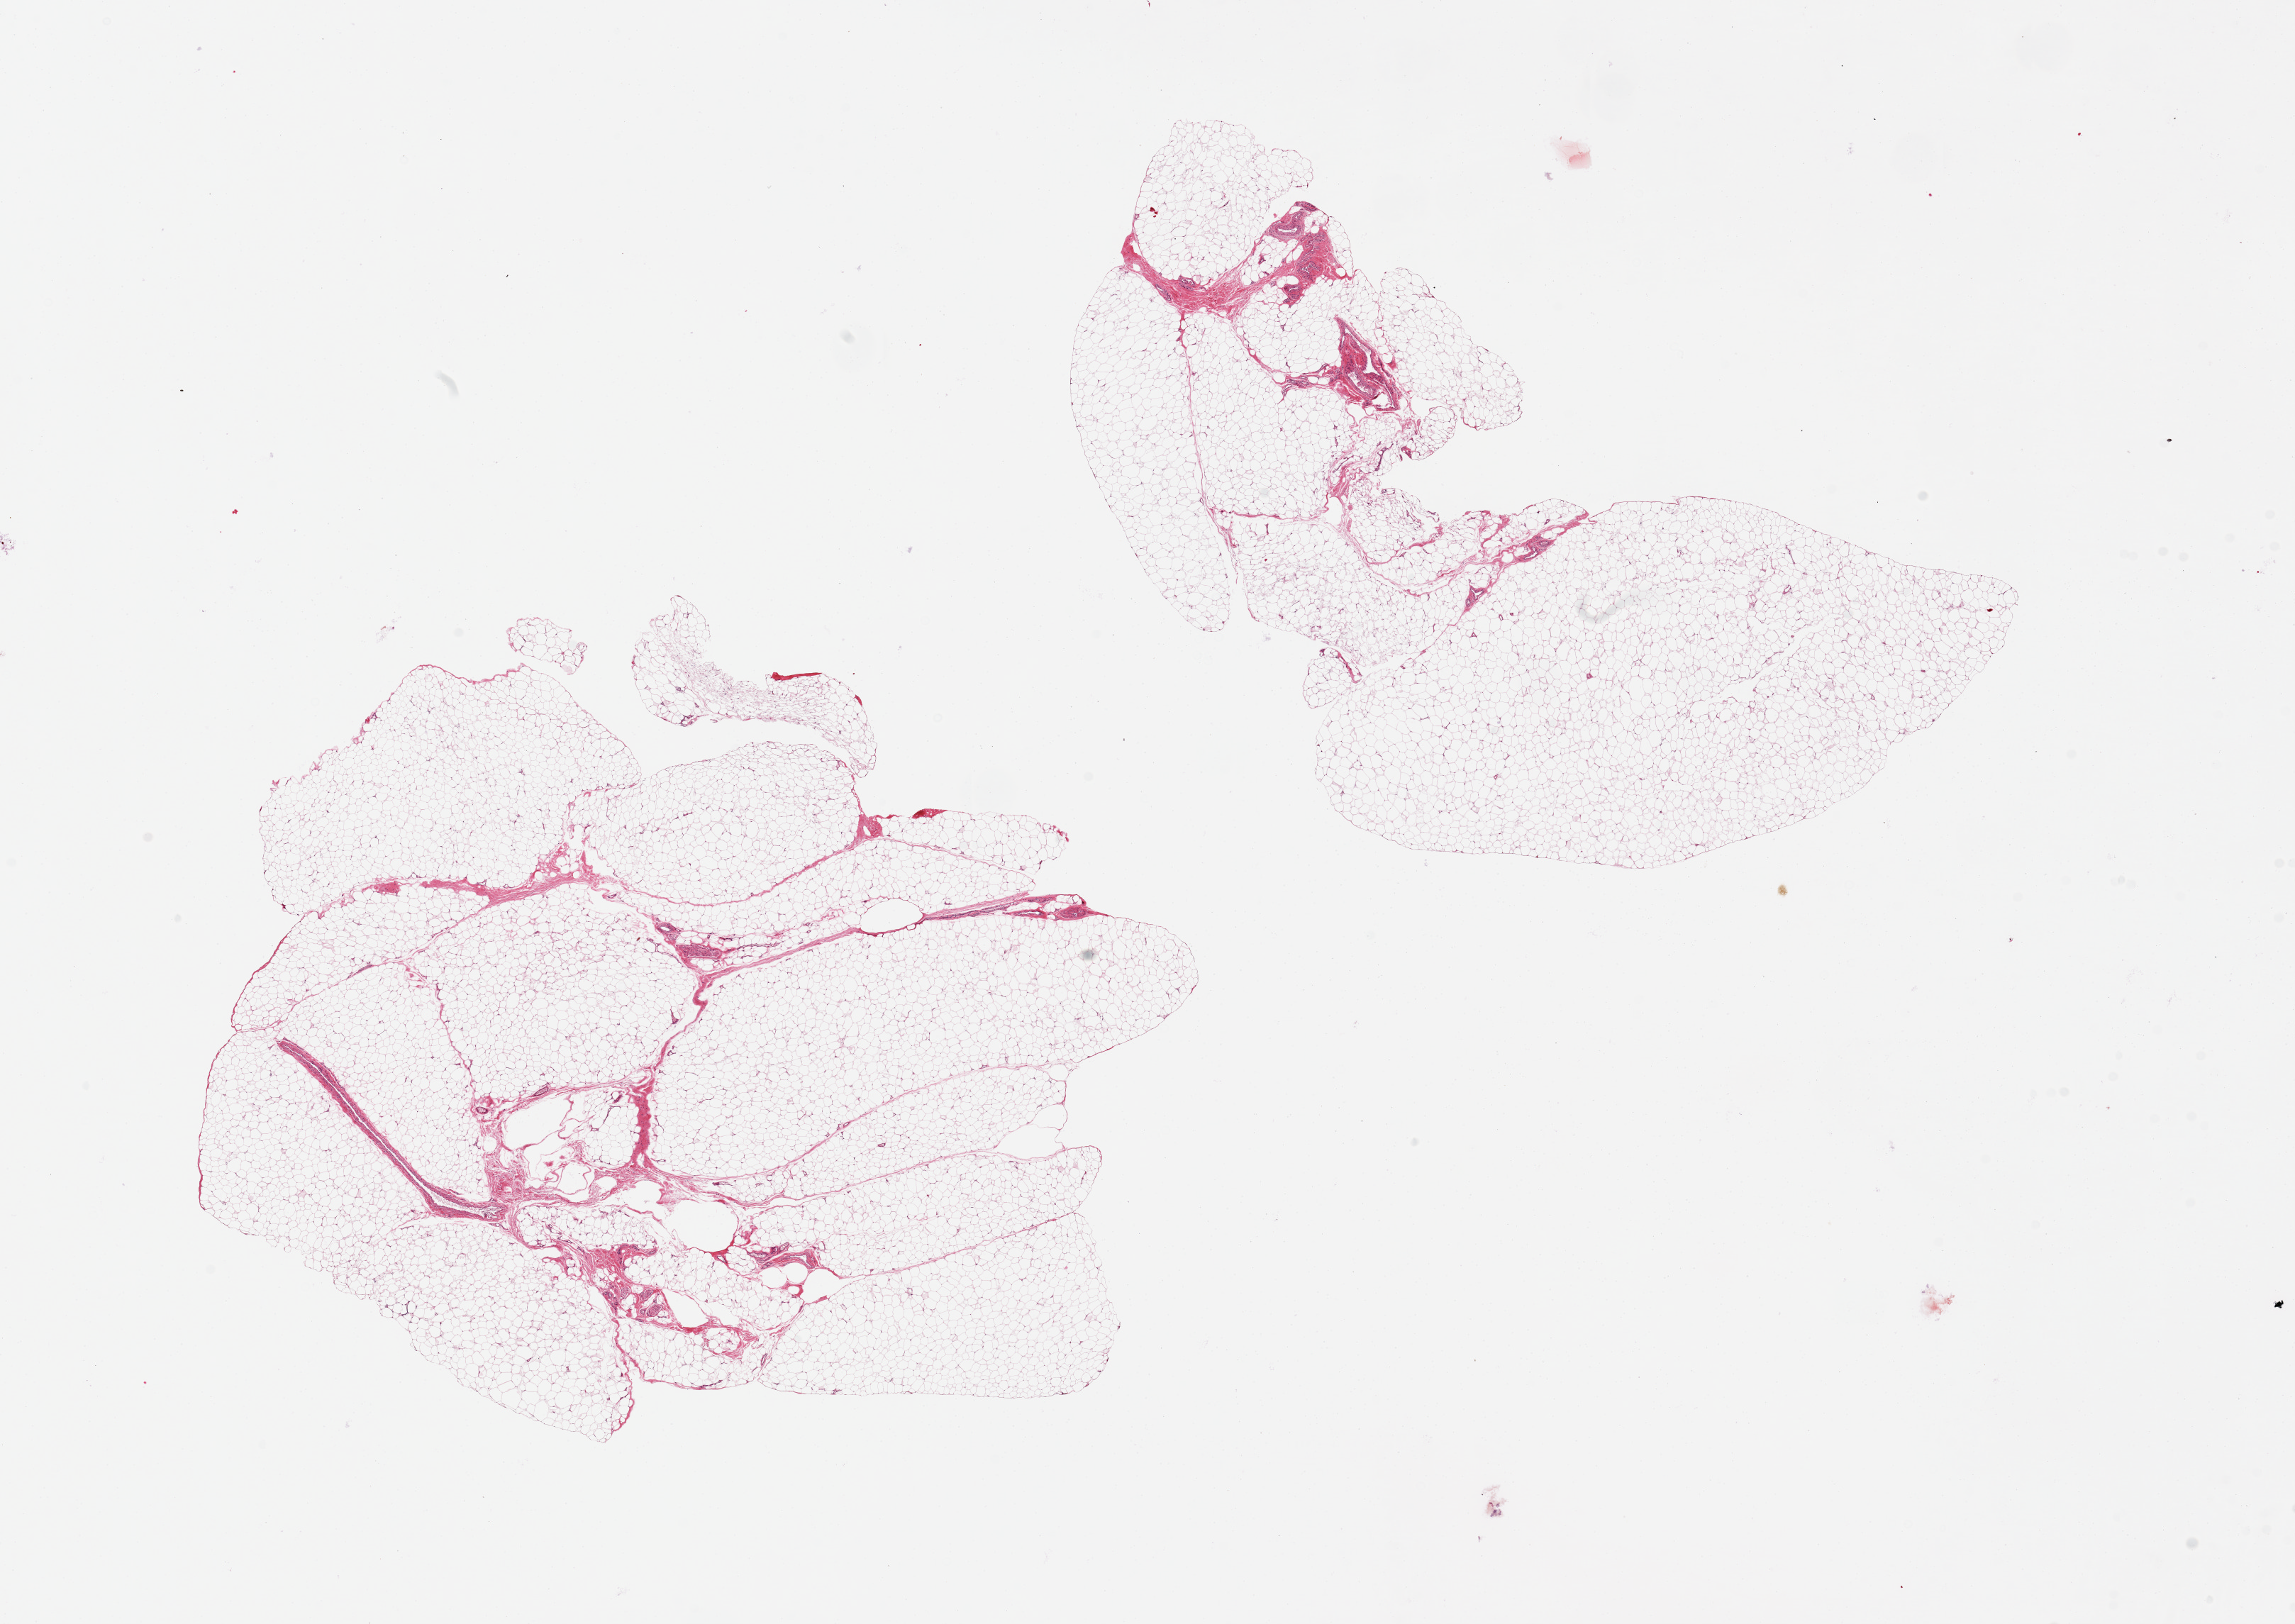
Haematoxylin and eosin whole-slide image — low-resolution overview of the scanned area, about 25.6 x 18.1 mm (slide scanned at 20x); PAXgene-fixed, paraffin-embedded tissue; sampled site (target tissue): adipose tissue; tissue donor sample.
Pathologist's review note for this sample: 2 pieces 10 x 5 and 11 x 9 mm. No fixation artifacts.